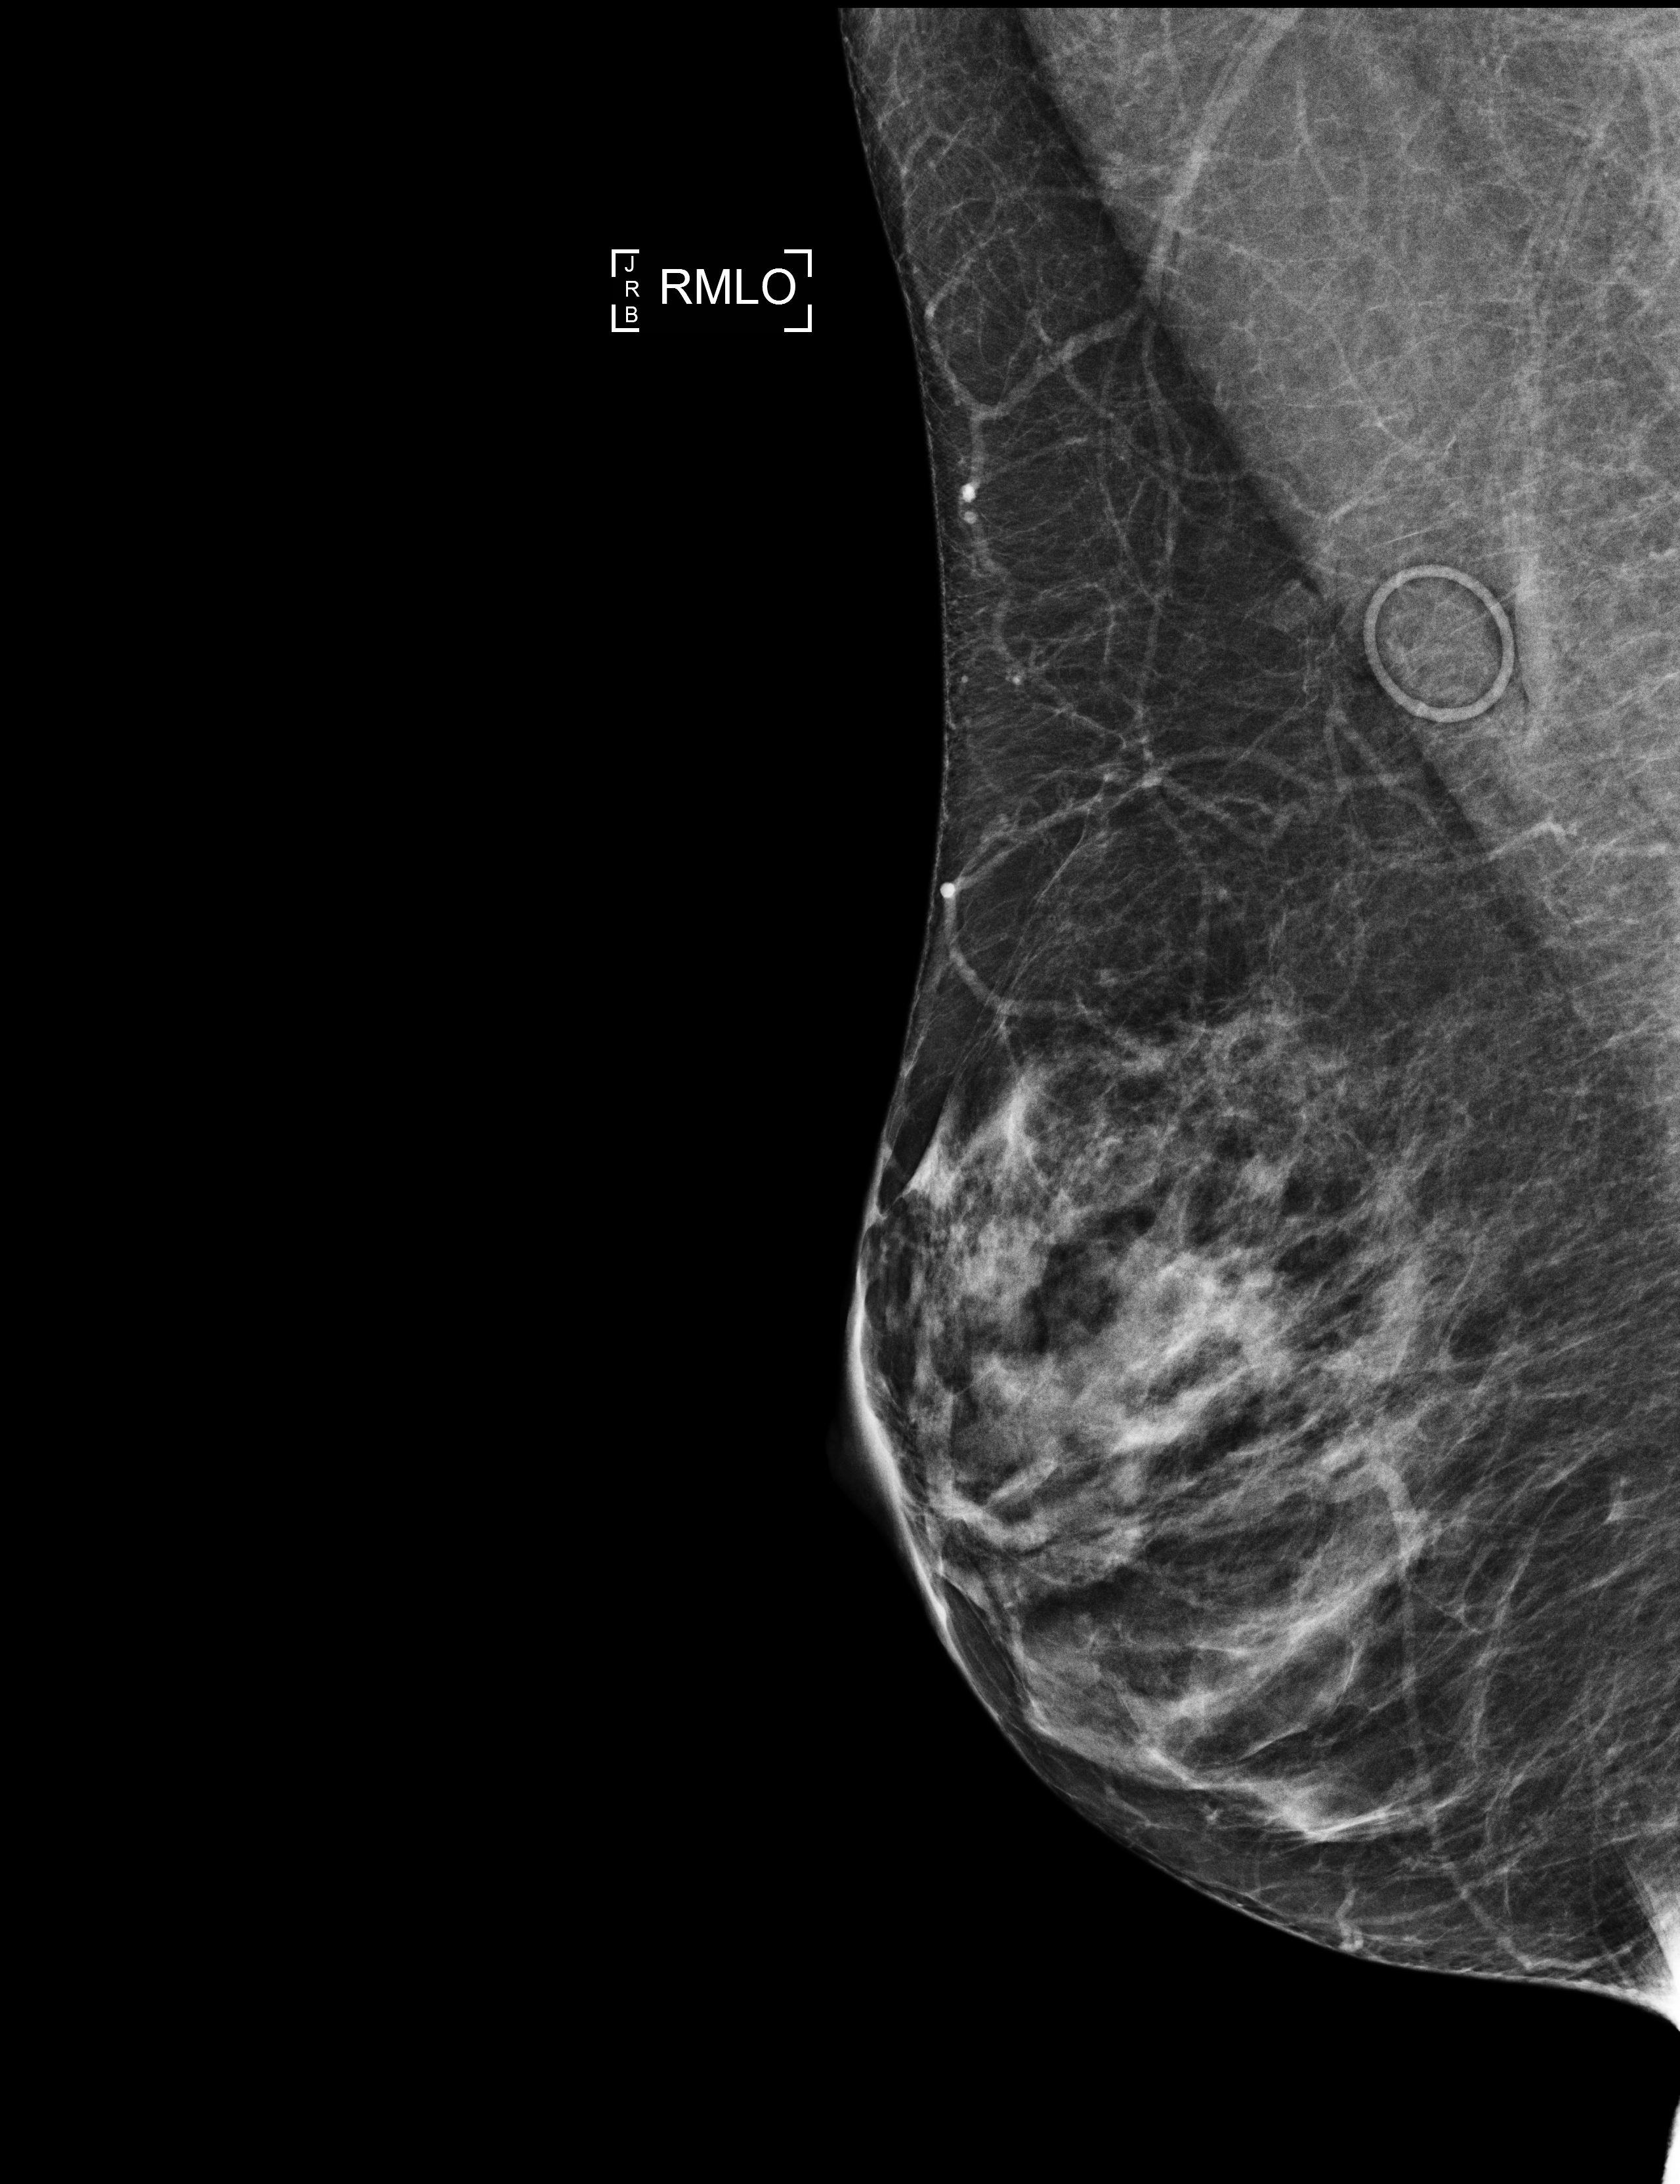
Screening examination, compressed breast thickness 41 mm, system: Selenia Dimensions. Patient: female, 60 years.
Image type: full-field digital mammogram. Breast: right. Projection: MLO view.